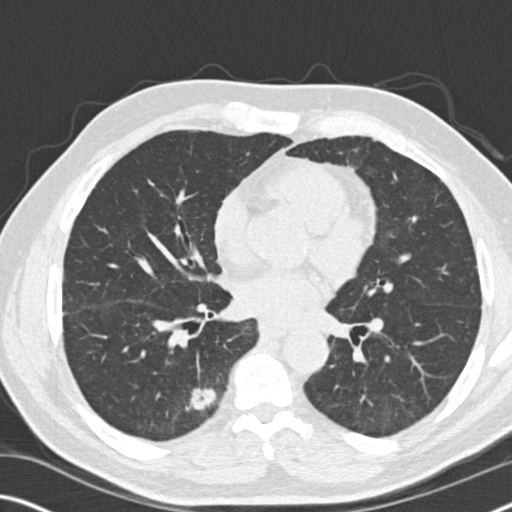
Low-dose screening chest CT, one axial slice. Slice 81 of 169 in the series (ordered by position). Reconstruction kernel B30f. 120 kVp. Lung window (W 1500 / L -600 HU). 512 × 512 image matrix.
Annotated regions visible in this slice (outlined manually by an expert reader):
- lesion 1 (tumor, lower lobe of right lung): bounding box (x1, y1, x2, y2) in pixels: (189, 388, 217, 411)